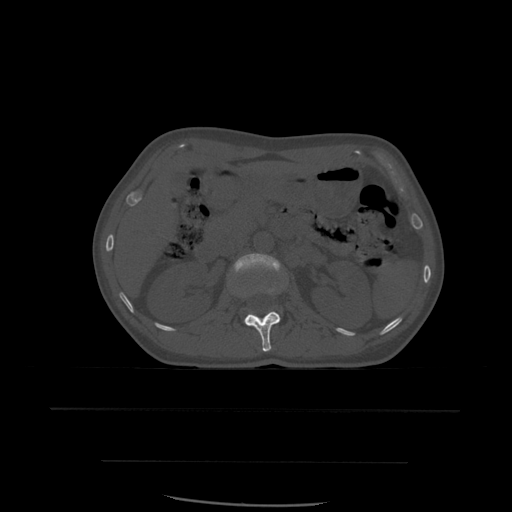
CT including the spine, one axial slice; position 240 of 574 along the scan axis; bone window (W 1800 / L 400 HU); 1.25 mm slice thickness; 512 × 512 image matrix, field of view 392 × 392 mm. Patient age 48 years. From the clinical record (not read from this slice): primary cancer: lung; vertebrae with lytic lesions (as recorded): T11.
Annotated regions visible in this slice (semi-automatic segmentation, software-assisted and operator-edited):
- L1 vertebra: bounding box <244,312,281,352> (left, top, right, bottom; pixels)
- L2 vertebra: <233,254,284,292>